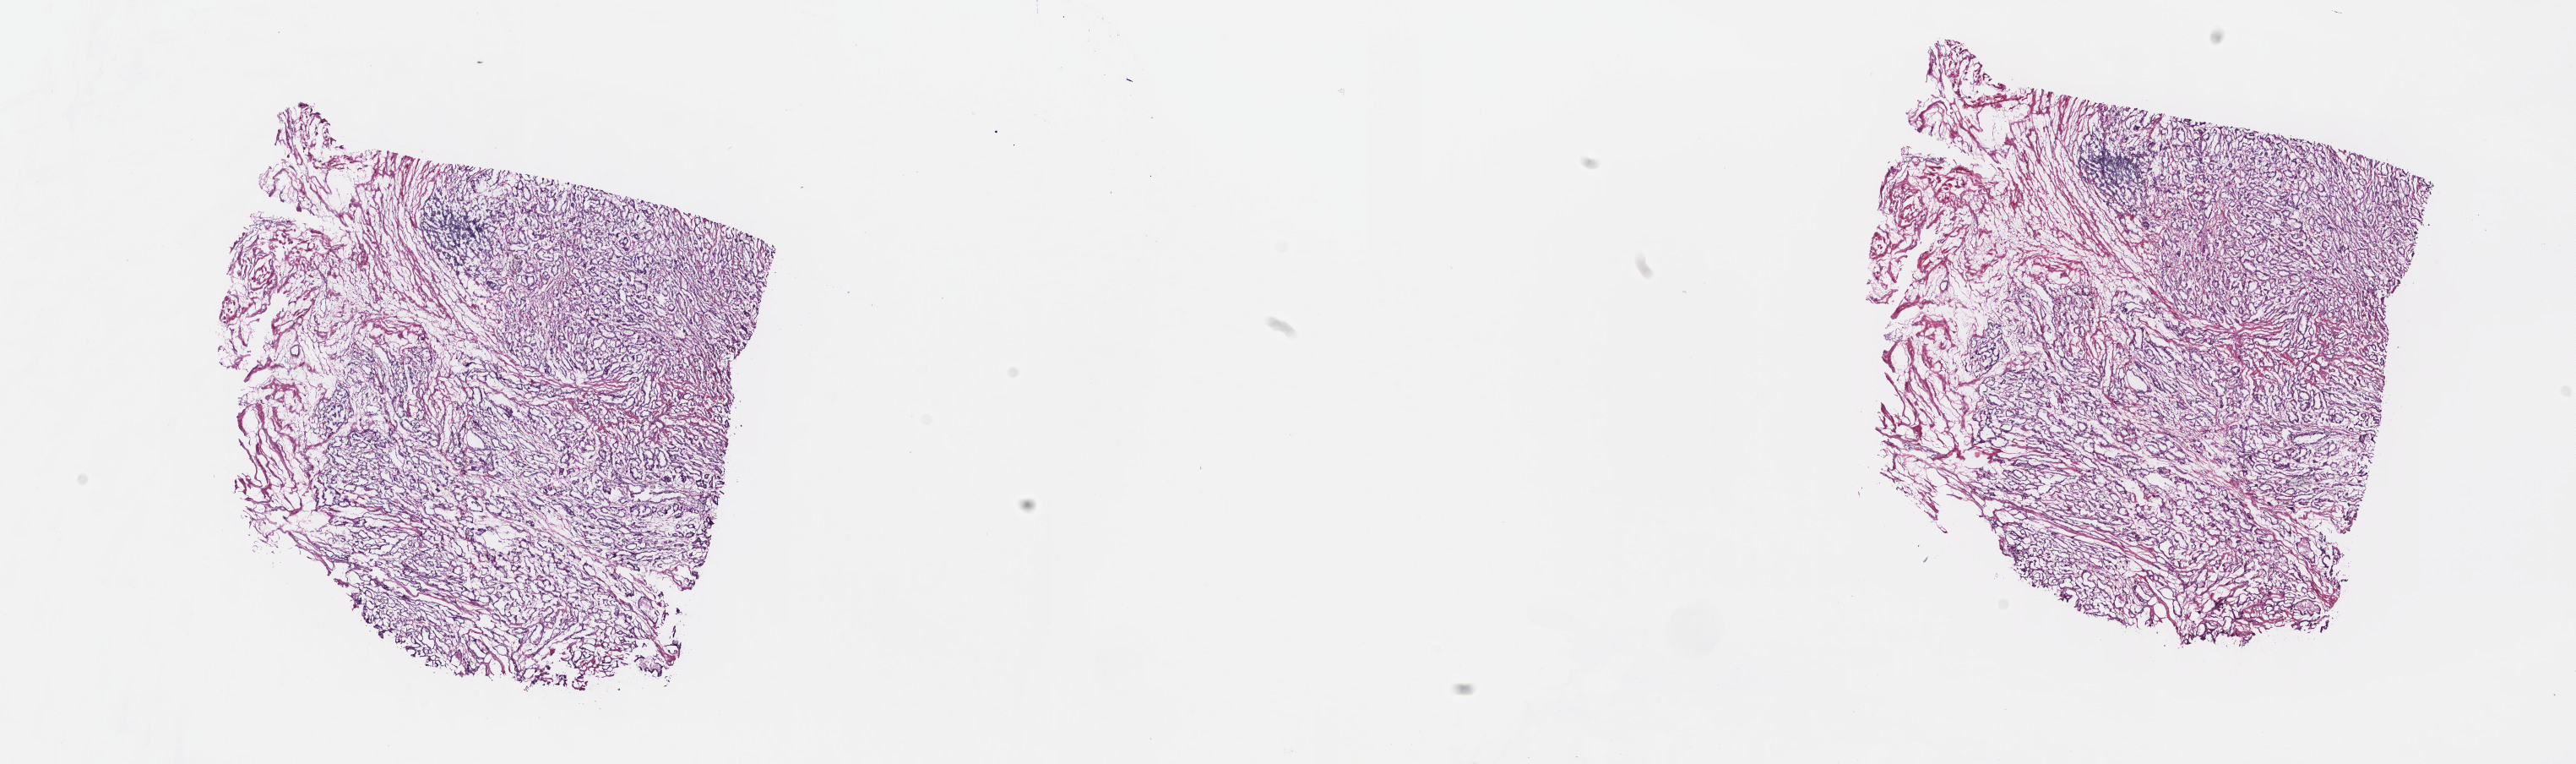
Digitized H&E-stained tissue section (whole slide) — a low-resolution overview of the entire scanned area, about 24.7 x 7.3 mm. Frozen section from the top of the tissue portion. Prostate, primary tumour sample. Male, age 56 years at initial diagnosis. Gleason score: 6 (3+3). Composition of this section per pathologist review: tumour cells 80%, tumour nuclei 90%, normal cells 0%, stromal cells 20%, necrosis 0%. Infiltration values recorded for this section: lymphocyte infiltration 0%, monocyte infiltration 0%, neutrophil infiltration 0%.
* diagnosis: Adenocarcinoma, NOS (prostate gland)
* laterality: bilateral
* lymph nodes positive (case pathology): 0 of 18 examined